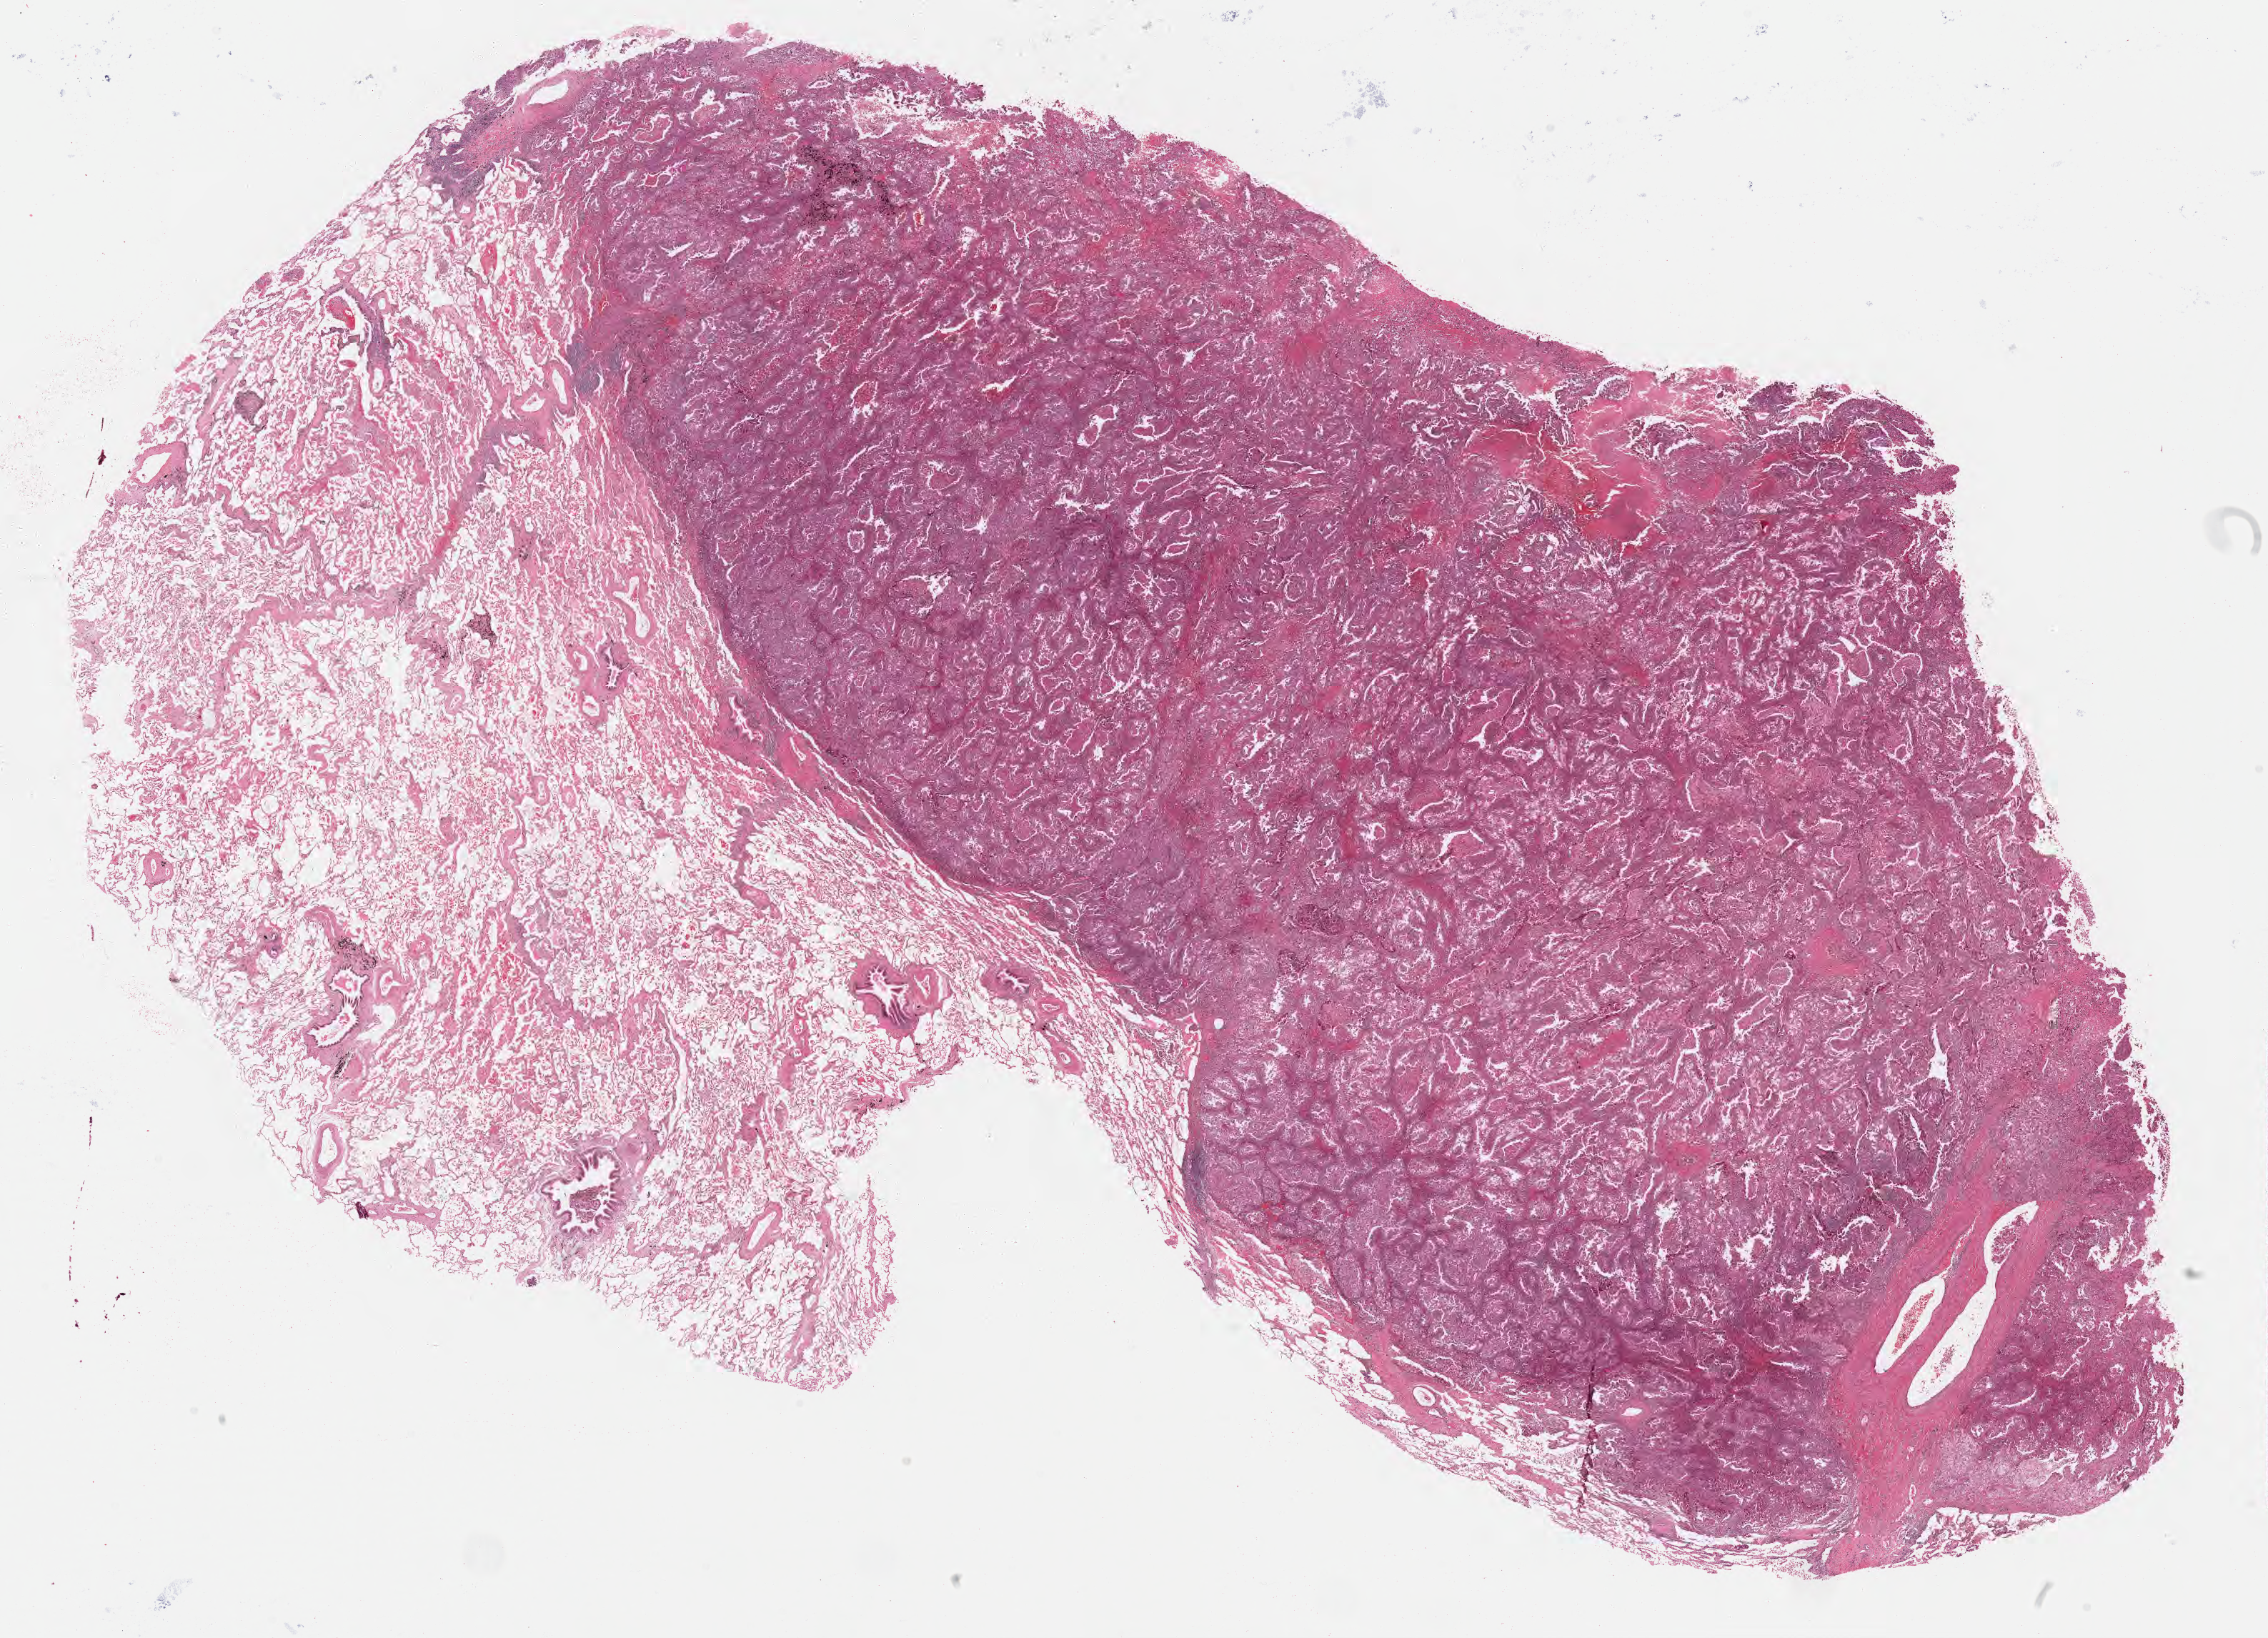
Whole-slide image, hematoxylin and eosin (H&E) stain, low-resolution overview of the scanned area, about 25.7 x 18.5 mm, FFPE section, specimen: primary tumor, anatomic site: upper lobe of left lung. Female patient, aged 79. Pathologist review of this section (percent, as recorded): tumor cells 70%, tumor nuclei 70%, stromal cells 25%, necrosis 1%, normal cells 4%. Inflammatory infiltration, as recorded: lymphocyte infiltration 4%, monocyte infiltration 4%, neutrophil infiltration 8%.
AJCC pathologic stage: Stage IIA. Diagnosis: Adenocarcinoma, NOS.